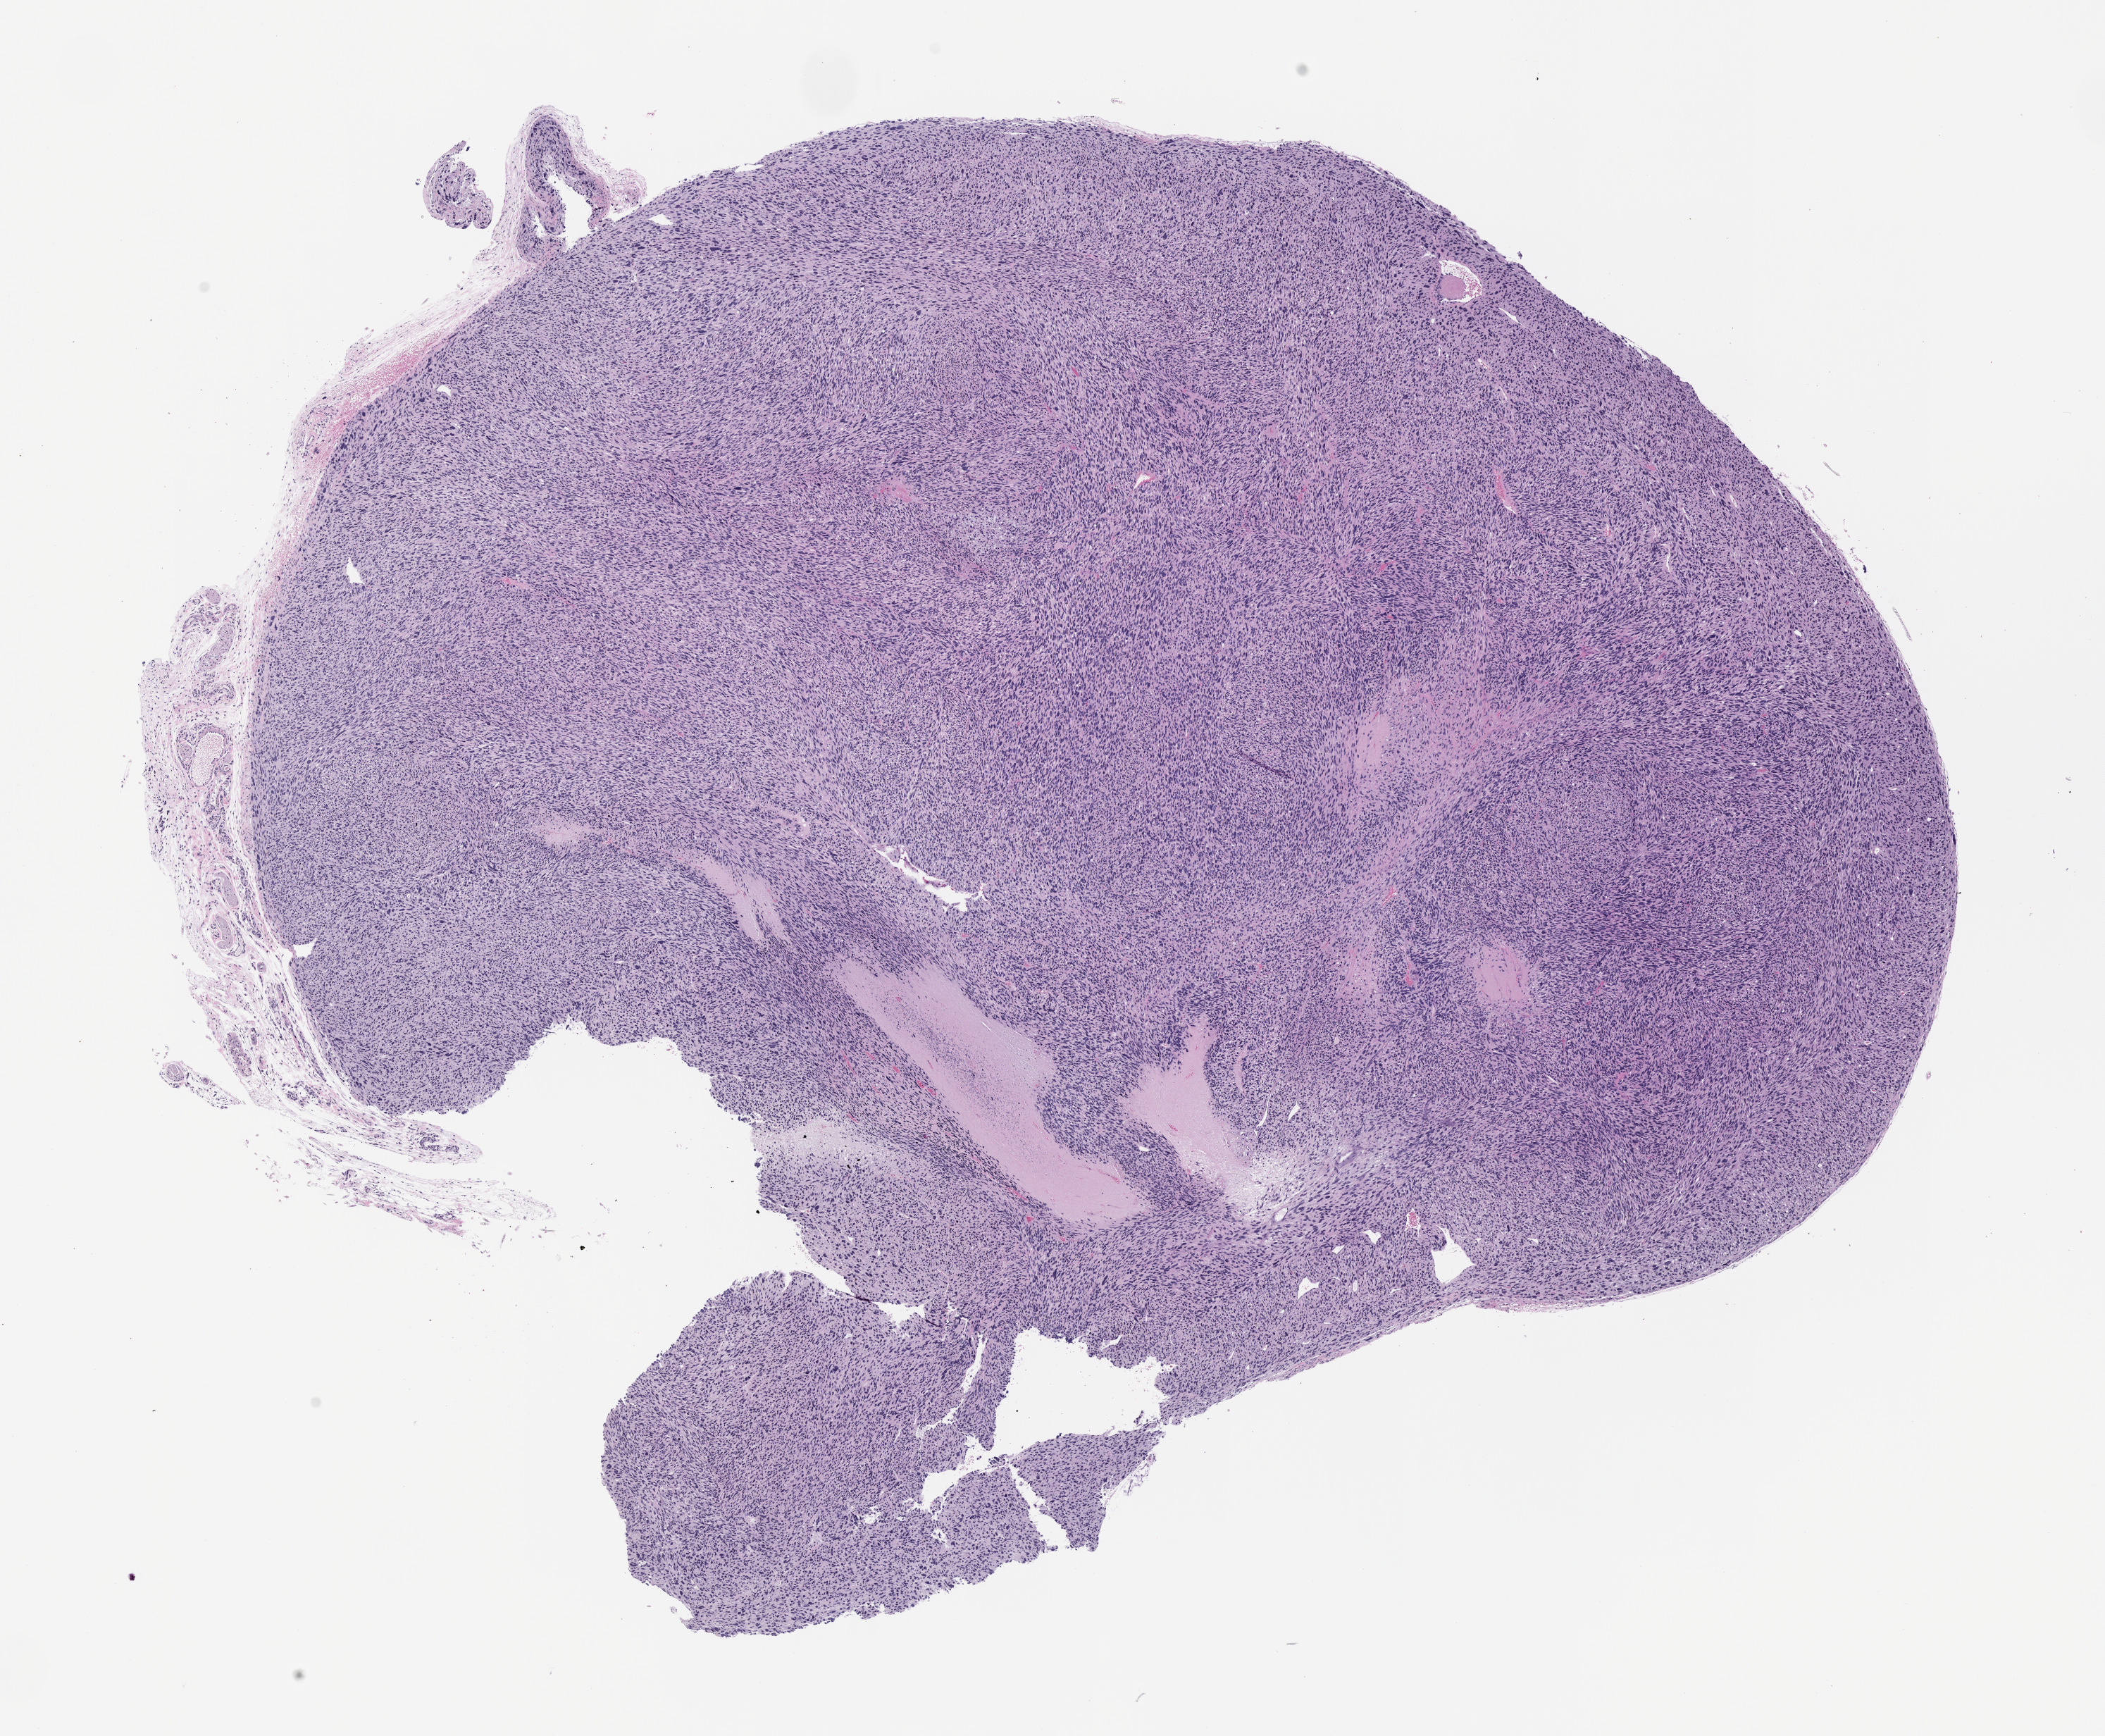
Haematoxylin and eosin whole-slide image of a patient-derived xenograft (PDX) tumor grown in a mouse, passage 1 — a low-resolution overview of the entire scanned area, about 12.0 x 9.9 mm. Formalin-fixed, paraffin-embedded (FFPE) tissue. Originating tumor site category: musculoskeletal.
Originating patient diagnosis: Leiomyosarcoma.